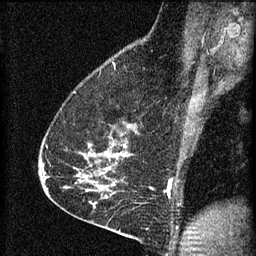
Breast MRI (dynamic contrast-enhanced), one sagittal slice. Position 43 of 60 along the scan axis. 3 images stored at this slice position (order not interpretable as contrast timing). 1.5 T. TE 4.2 ms, TR 8.2 ms. 2 mm slice thickness. 256 × 256 image matrix, field of view 180 × 180 mm. Patient: female, 59 years.
Annotated regions visible in this slice (semi-automatically segmented with operator editing):
- analysis volume of interest (the breast-tissue region the enhancement analysis was run in; not a lesion): bounding box (x1, y1, x2, y2) in pixels: (64, 106, 134, 161)
- tumour enhancement mask (voxels above the 70 % enhancement threshold inside the analysis volume of interest): (91, 146, 126, 155)